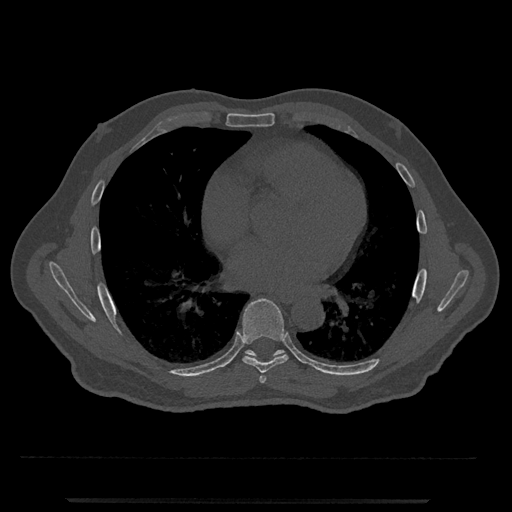
CT including the spine, one axial slice. Slice 670 of 797 in the series (ordered by position). Reconstruction kernel Br40s/3. 120 kVp. Bone window (W 1800 / L 400 HU). 0.5 mm slice thickness. 512 × 512 image matrix. Patient: male, 63 years. From the clinical record (not read from this slice): primary cancer: prostate.
Outlined on this slice (semi-automatic segmentation, software-assisted and operator-edited):
- T6 vertebra: bounding box (x1, y1, x2, y2) in pixels: (259, 375, 266, 383)
- T7 vertebra: (238, 298, 289, 373)
- T8 vertebra: (245, 350, 285, 357)